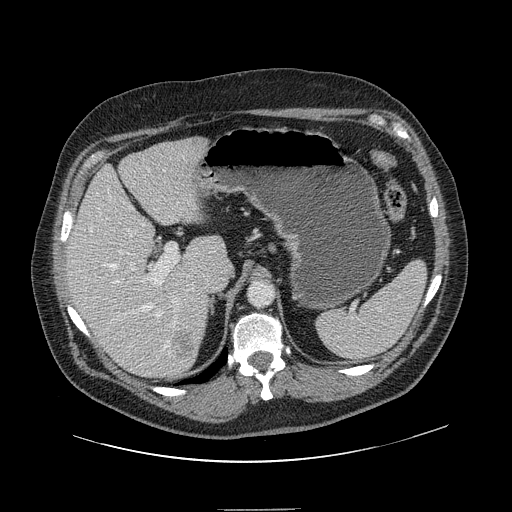
Contrast-enhanced abdominal CT, one axial slice; position 95 of 154 along the scan axis; intravenous contrast given; soft-tissue window (W 400 / L 40 HU); 2.5 mm slice thickness; 512 × 512 image matrix, field of view 451 × 451 mm. Male patient, age 61 years. Case-level facts recorded for this patient, not image findings: diagnosis: colorectal cancer liver metastases, imaged before liver resection; multiple liver metastases: yes; largest metastasis: 2.6 cm; disease in both lobes: yes.
Structures marked on this image (expert manual segmentation):
- hepatic veins: bounding box [x1, y1, x2, y2] px = [90, 209, 180, 350]
- liver: [68, 138, 226, 379]
- planned liver remnant (the part of the liver to remain after resection): [68, 146, 225, 364]
- portal vein (with intrahepatic branches): [107, 186, 179, 304]
- liver metastasis: [194, 142, 203, 152]
- liver metastasis: [178, 335, 195, 354]